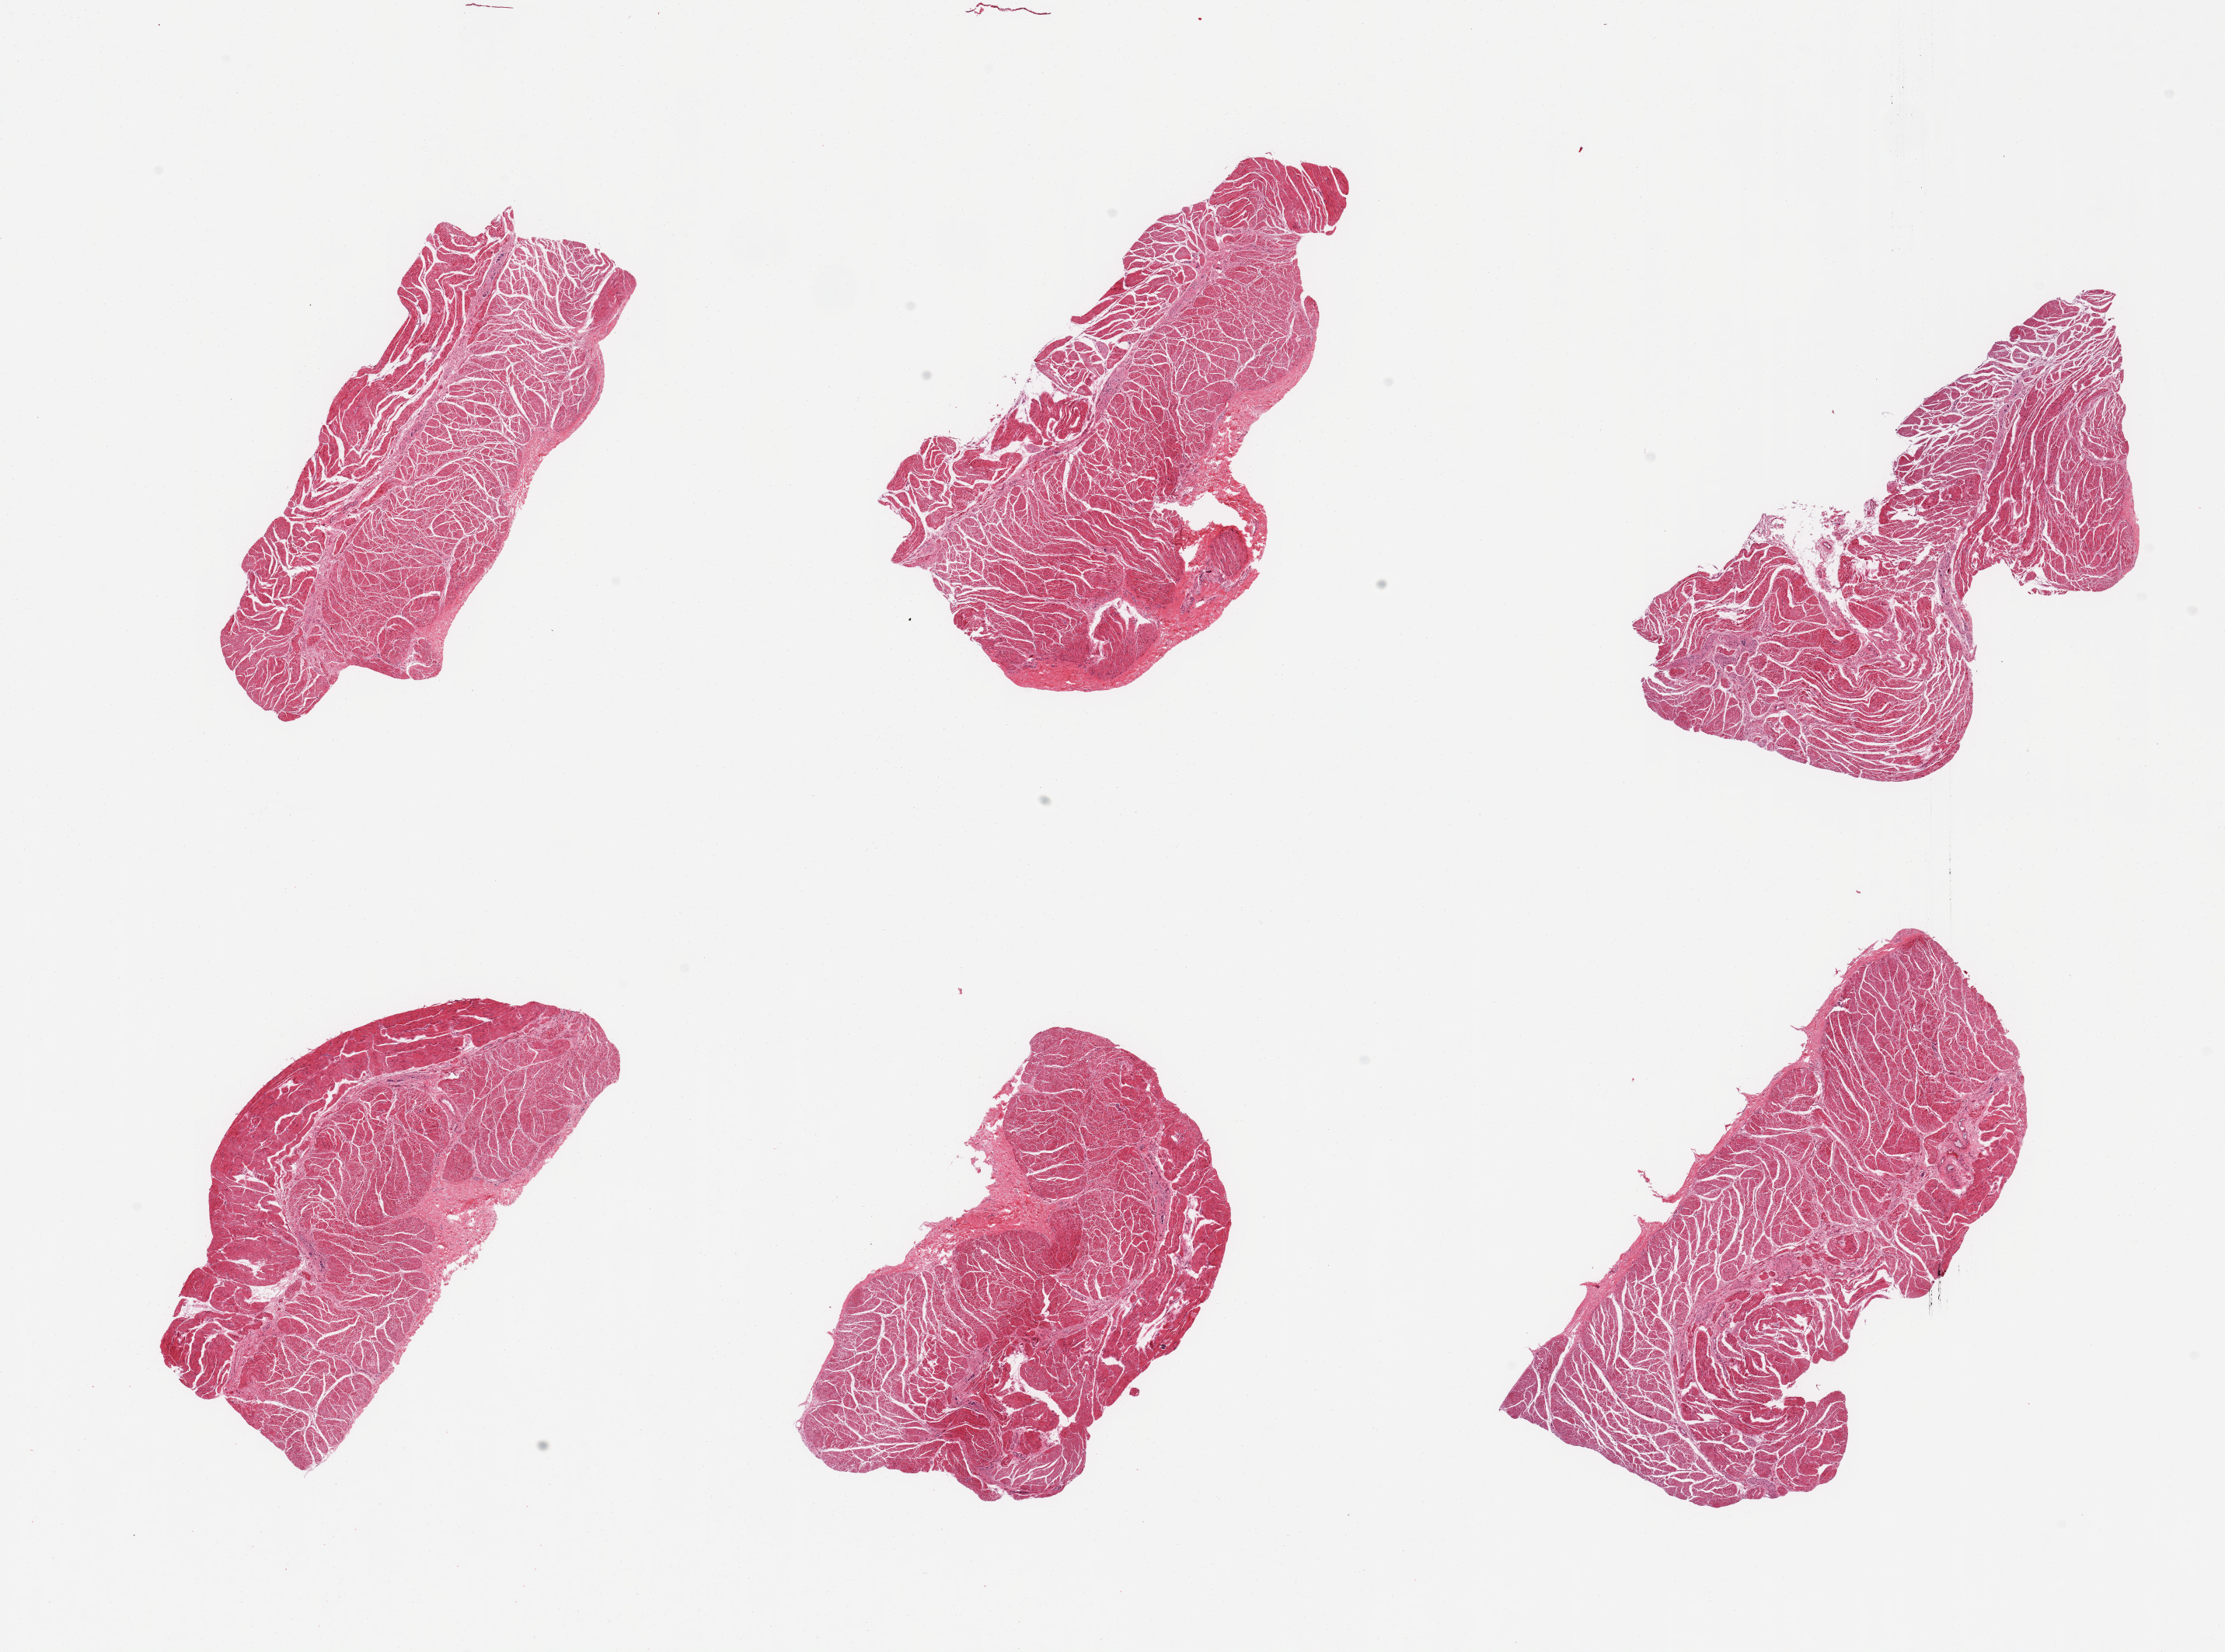
Digitized H&E-stained section — low-resolution overview of the scanned area, about 22.6 x 16.8 mm, PAXgene-fixed paraffin-embedded (PFPE) section, sampled site (target tissue): esophageal muscle, tissue donor sample. Donor sex: female.
Reviewer comment on this tissue sample: 6 pieces; well dissected muscle with minimal submucosa.